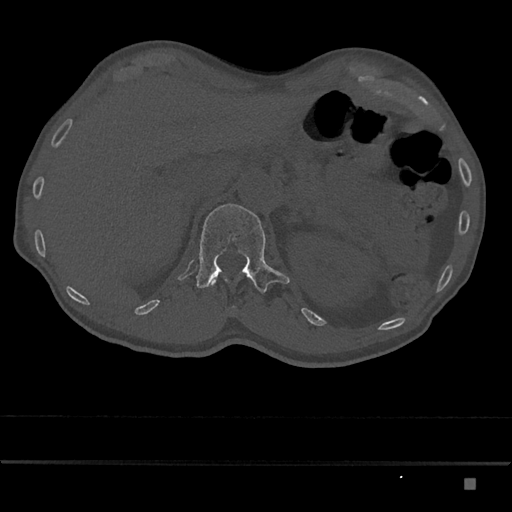
CT including the spine, one axial slice. Slice 560 of 797 in the series (ordered by position). Bone window (W 1800 / L 400 HU). 0.5 mm slice thickness. 512 × 512 image matrix. Patient: male, 72 years. From the clinical record (not read from this slice): primary cancer: prostate.
Structures marked on this image (semi-automatic segmentation, software-assisted and operator-edited):
- L1 vertebra: bounding box [x1, y1, x2, y2] px = [196, 204, 290, 293]
- T12 vertebra: [209, 278, 228, 286]